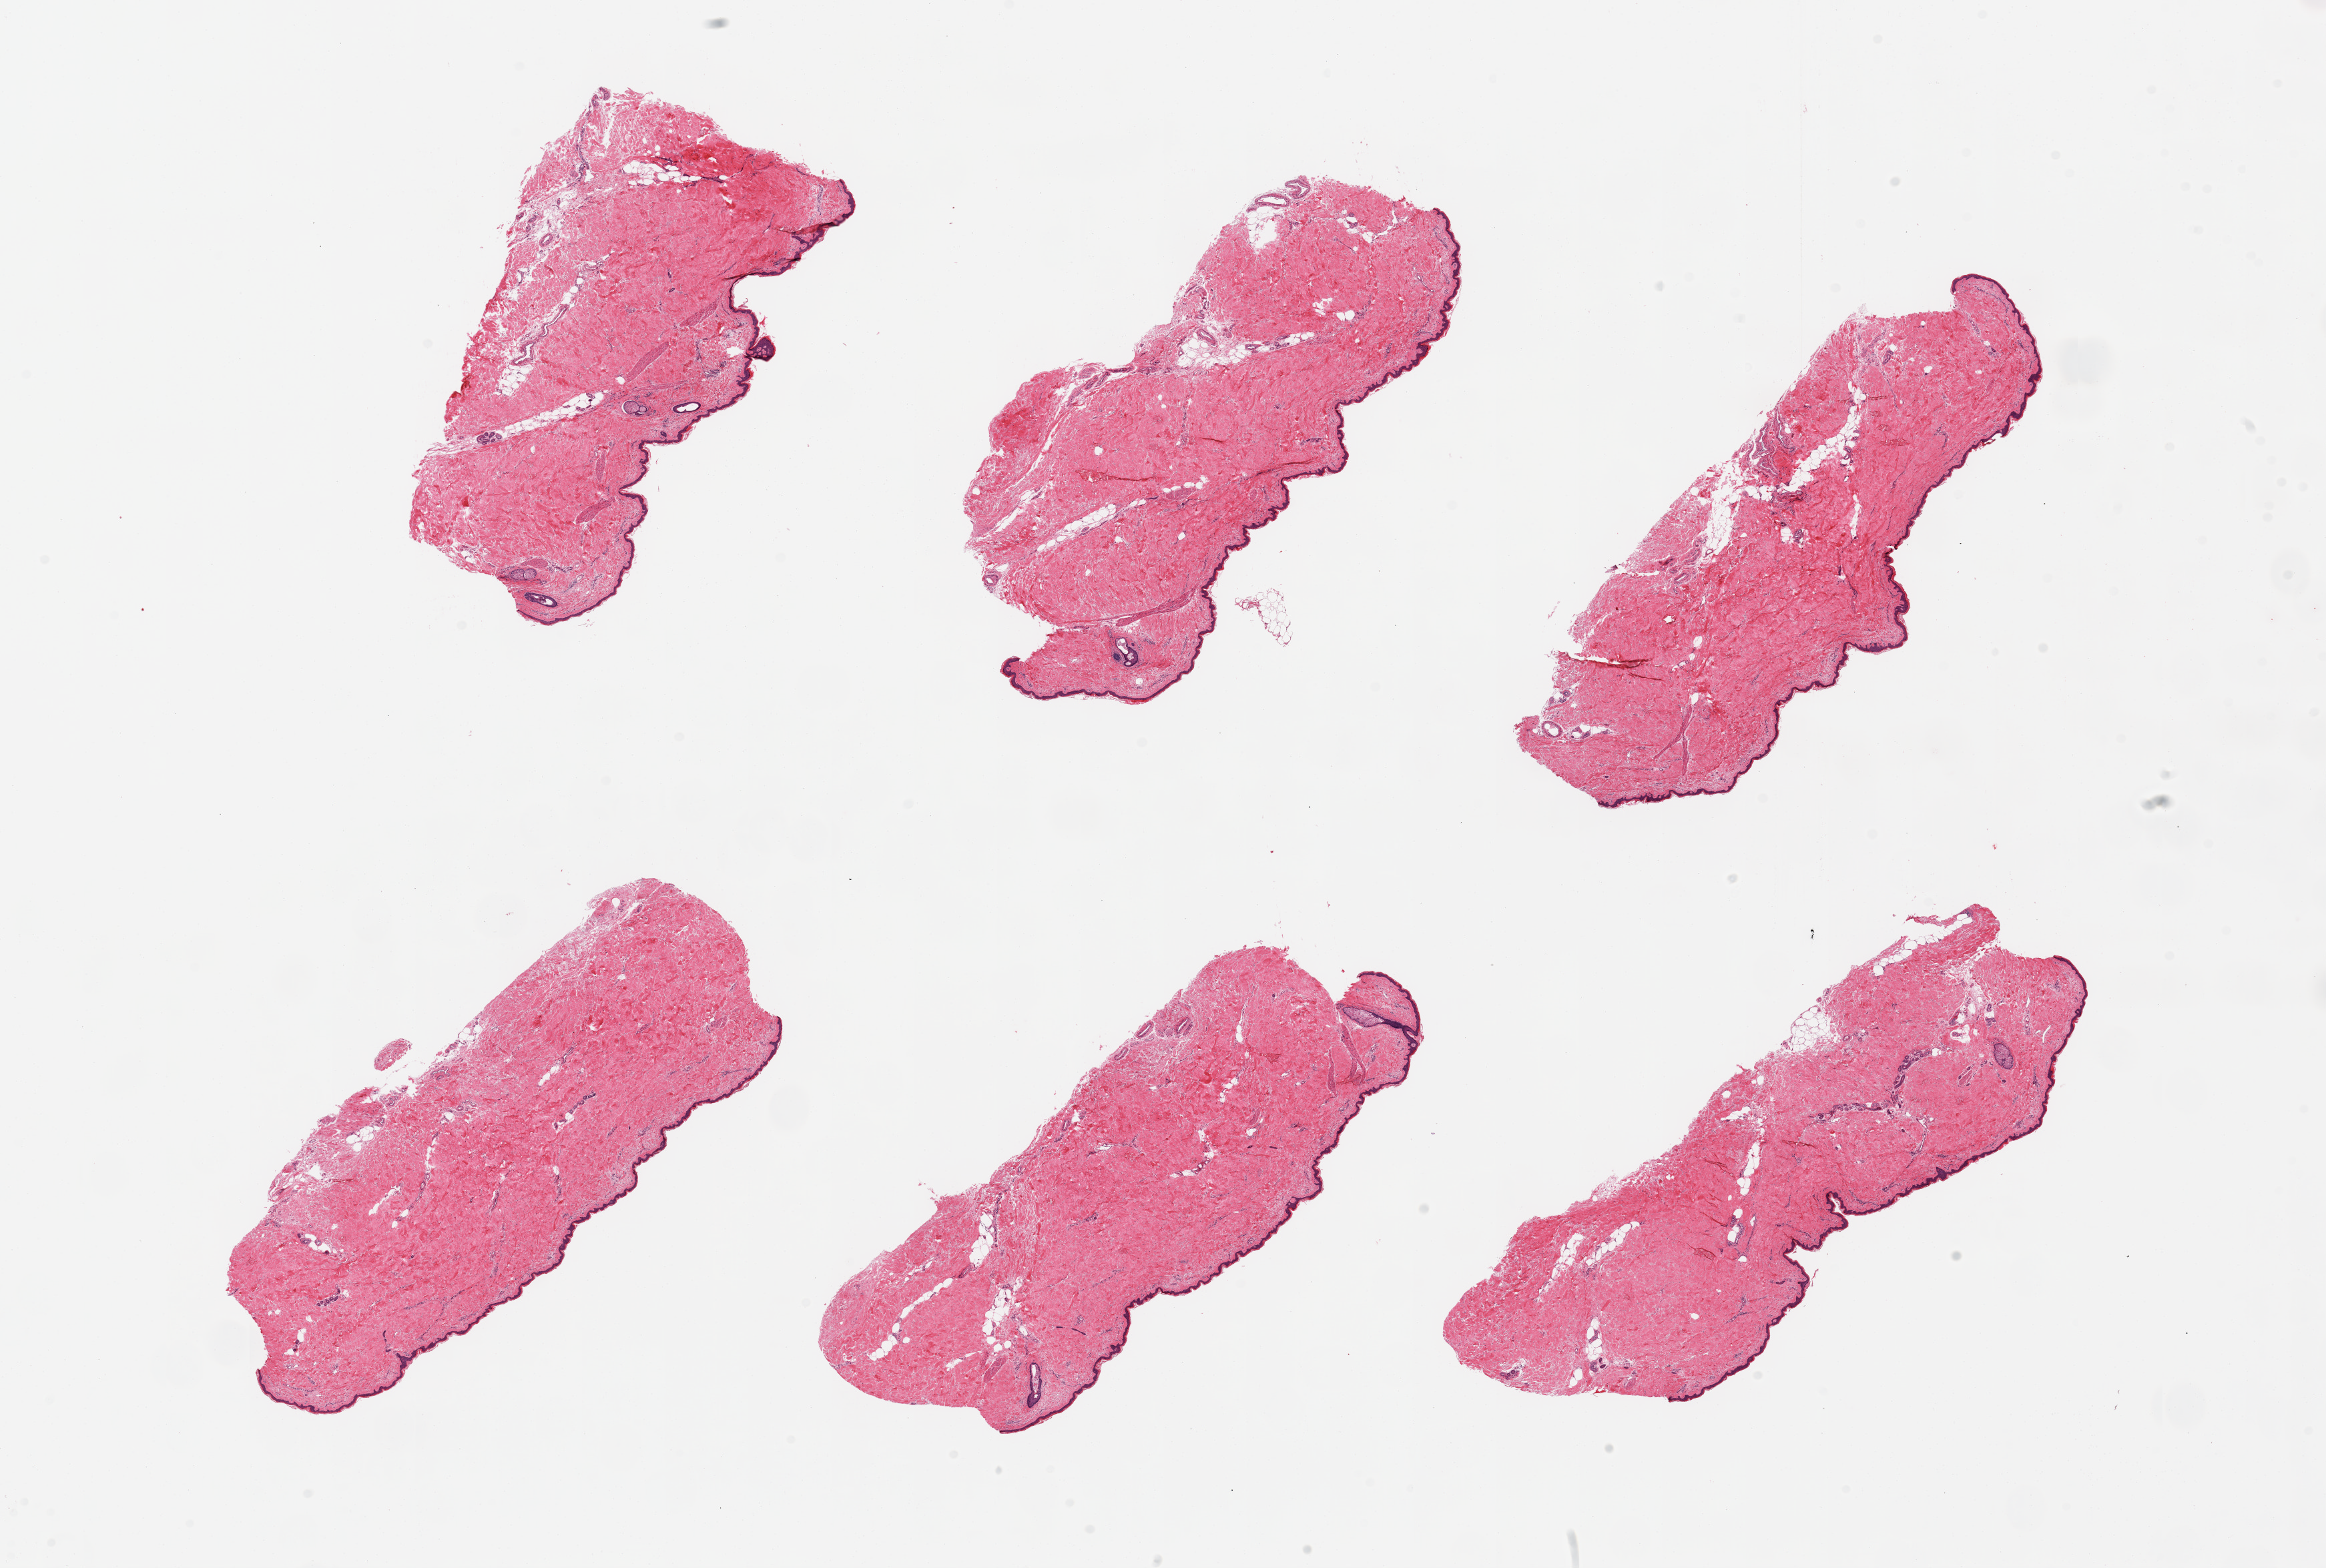
Whole-slide image, H&E stain — low-resolution overview of the scanned area, about 27.6 x 18.6 mm. PAXgene-fixed paraffin-embedded (PFPE) section. Target tissue: skin of lower leg. Tissue donor sample. Female donor.
Pathologist's review note for this sample: 6 pieces; well trimmed; 5% intradermal fat.